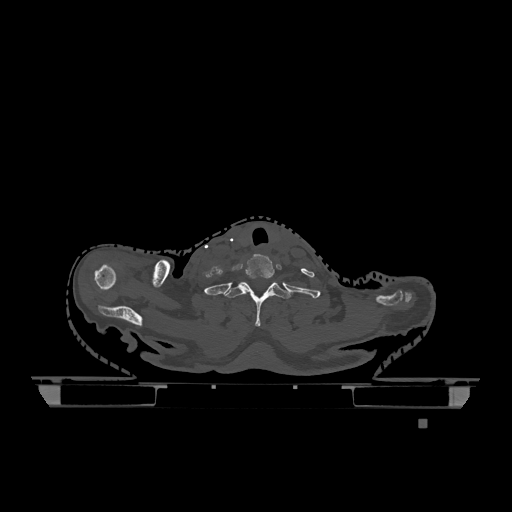
CT including the spine, one axial slice; position 1009 of 1317 along the scan axis; bone window (W 1800 / L 400 HU); 0.5 mm slice thickness; 512 × 512 image matrix. Female patient, age 74 years. Case-level facts recorded for this patient, not image findings: primary cancer: lung; vertebrae with lytic lesions (as recorded): T1, T4, T5, T6, L4, L5.
Structures marked on this image (semi-automatic segmentation, software-assisted and operator-edited):
- T1 vertebra: bounding box (x1, y1, x2, y2) in pixels: (223, 282, 291, 327)